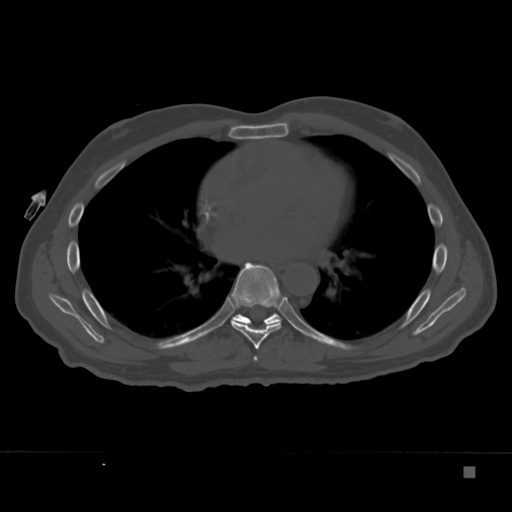
CT including the spine, one axial slice. Slice 218 of 332 in the series (ordered by position). Bone window (W 1800 / L 400 HU). 1.5 mm slice thickness. 512 × 512 image matrix. Patient: male, 72 years. From the clinical record (not read from this slice): primary cancer: skeletal.
Annotated regions visible in this slice (semi-automatic segmentation, software-assisted and operator-edited):
- T6 vertebra: bounding box <253,356,258,362> (left, top, right, bottom; pixels)
- T7 vertebra: <230,262,283,350>
- T8 vertebra: <232,313,301,332>